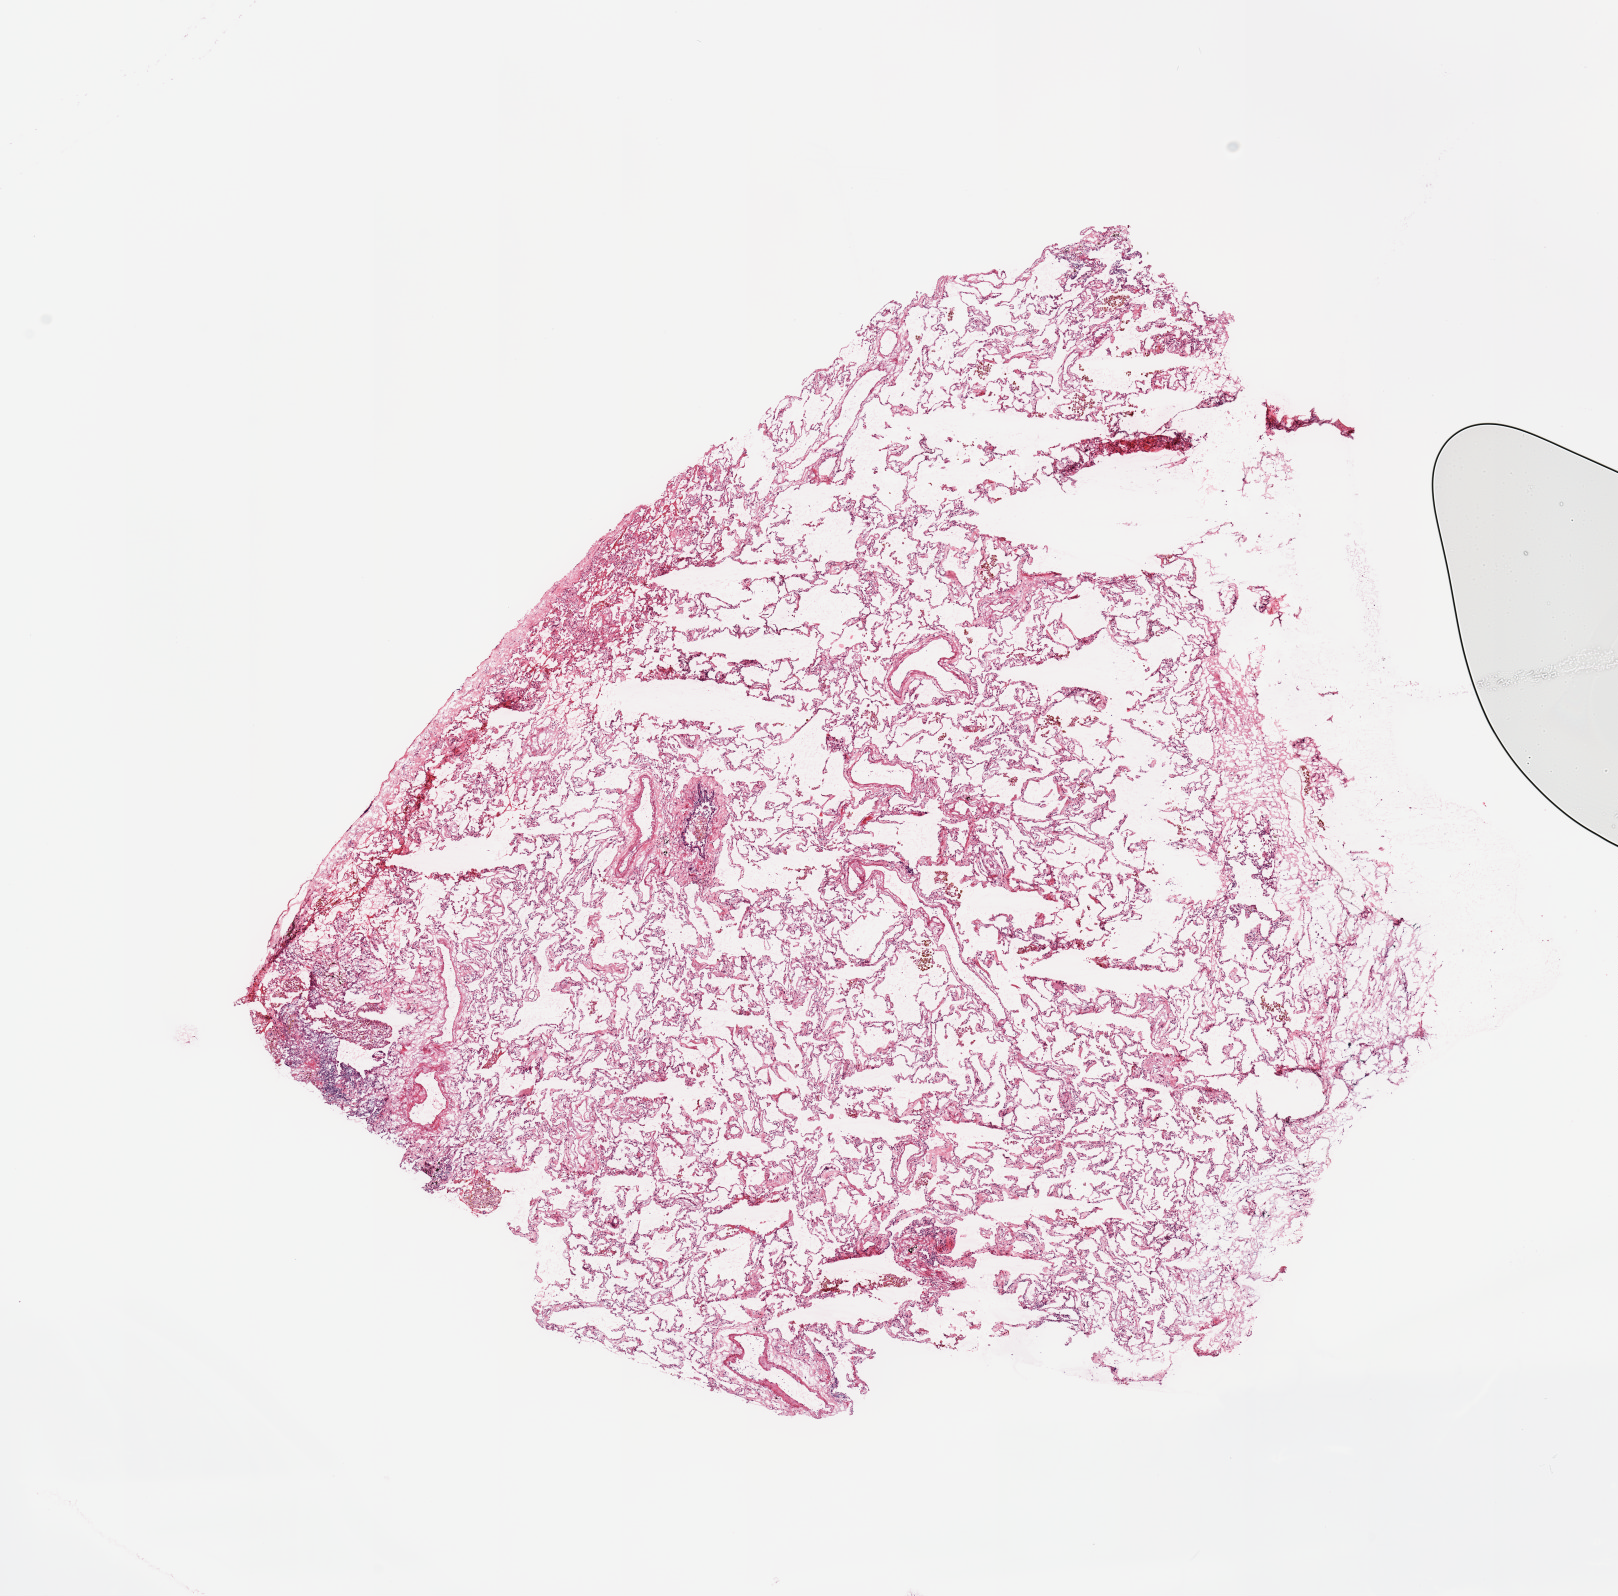
H&E whole-slide image — shown as a low-resolution overview of the whole scanned area (about 12.8 x 12.6 mm, slide scanned at 20x), normal (non-tumour) tissue sample, sampled site: lung. Female, 72 y/o.
This section: normal (non-tumour) tissue from the same patient. Patient diagnosis: Adenocarcinoma, NOS.